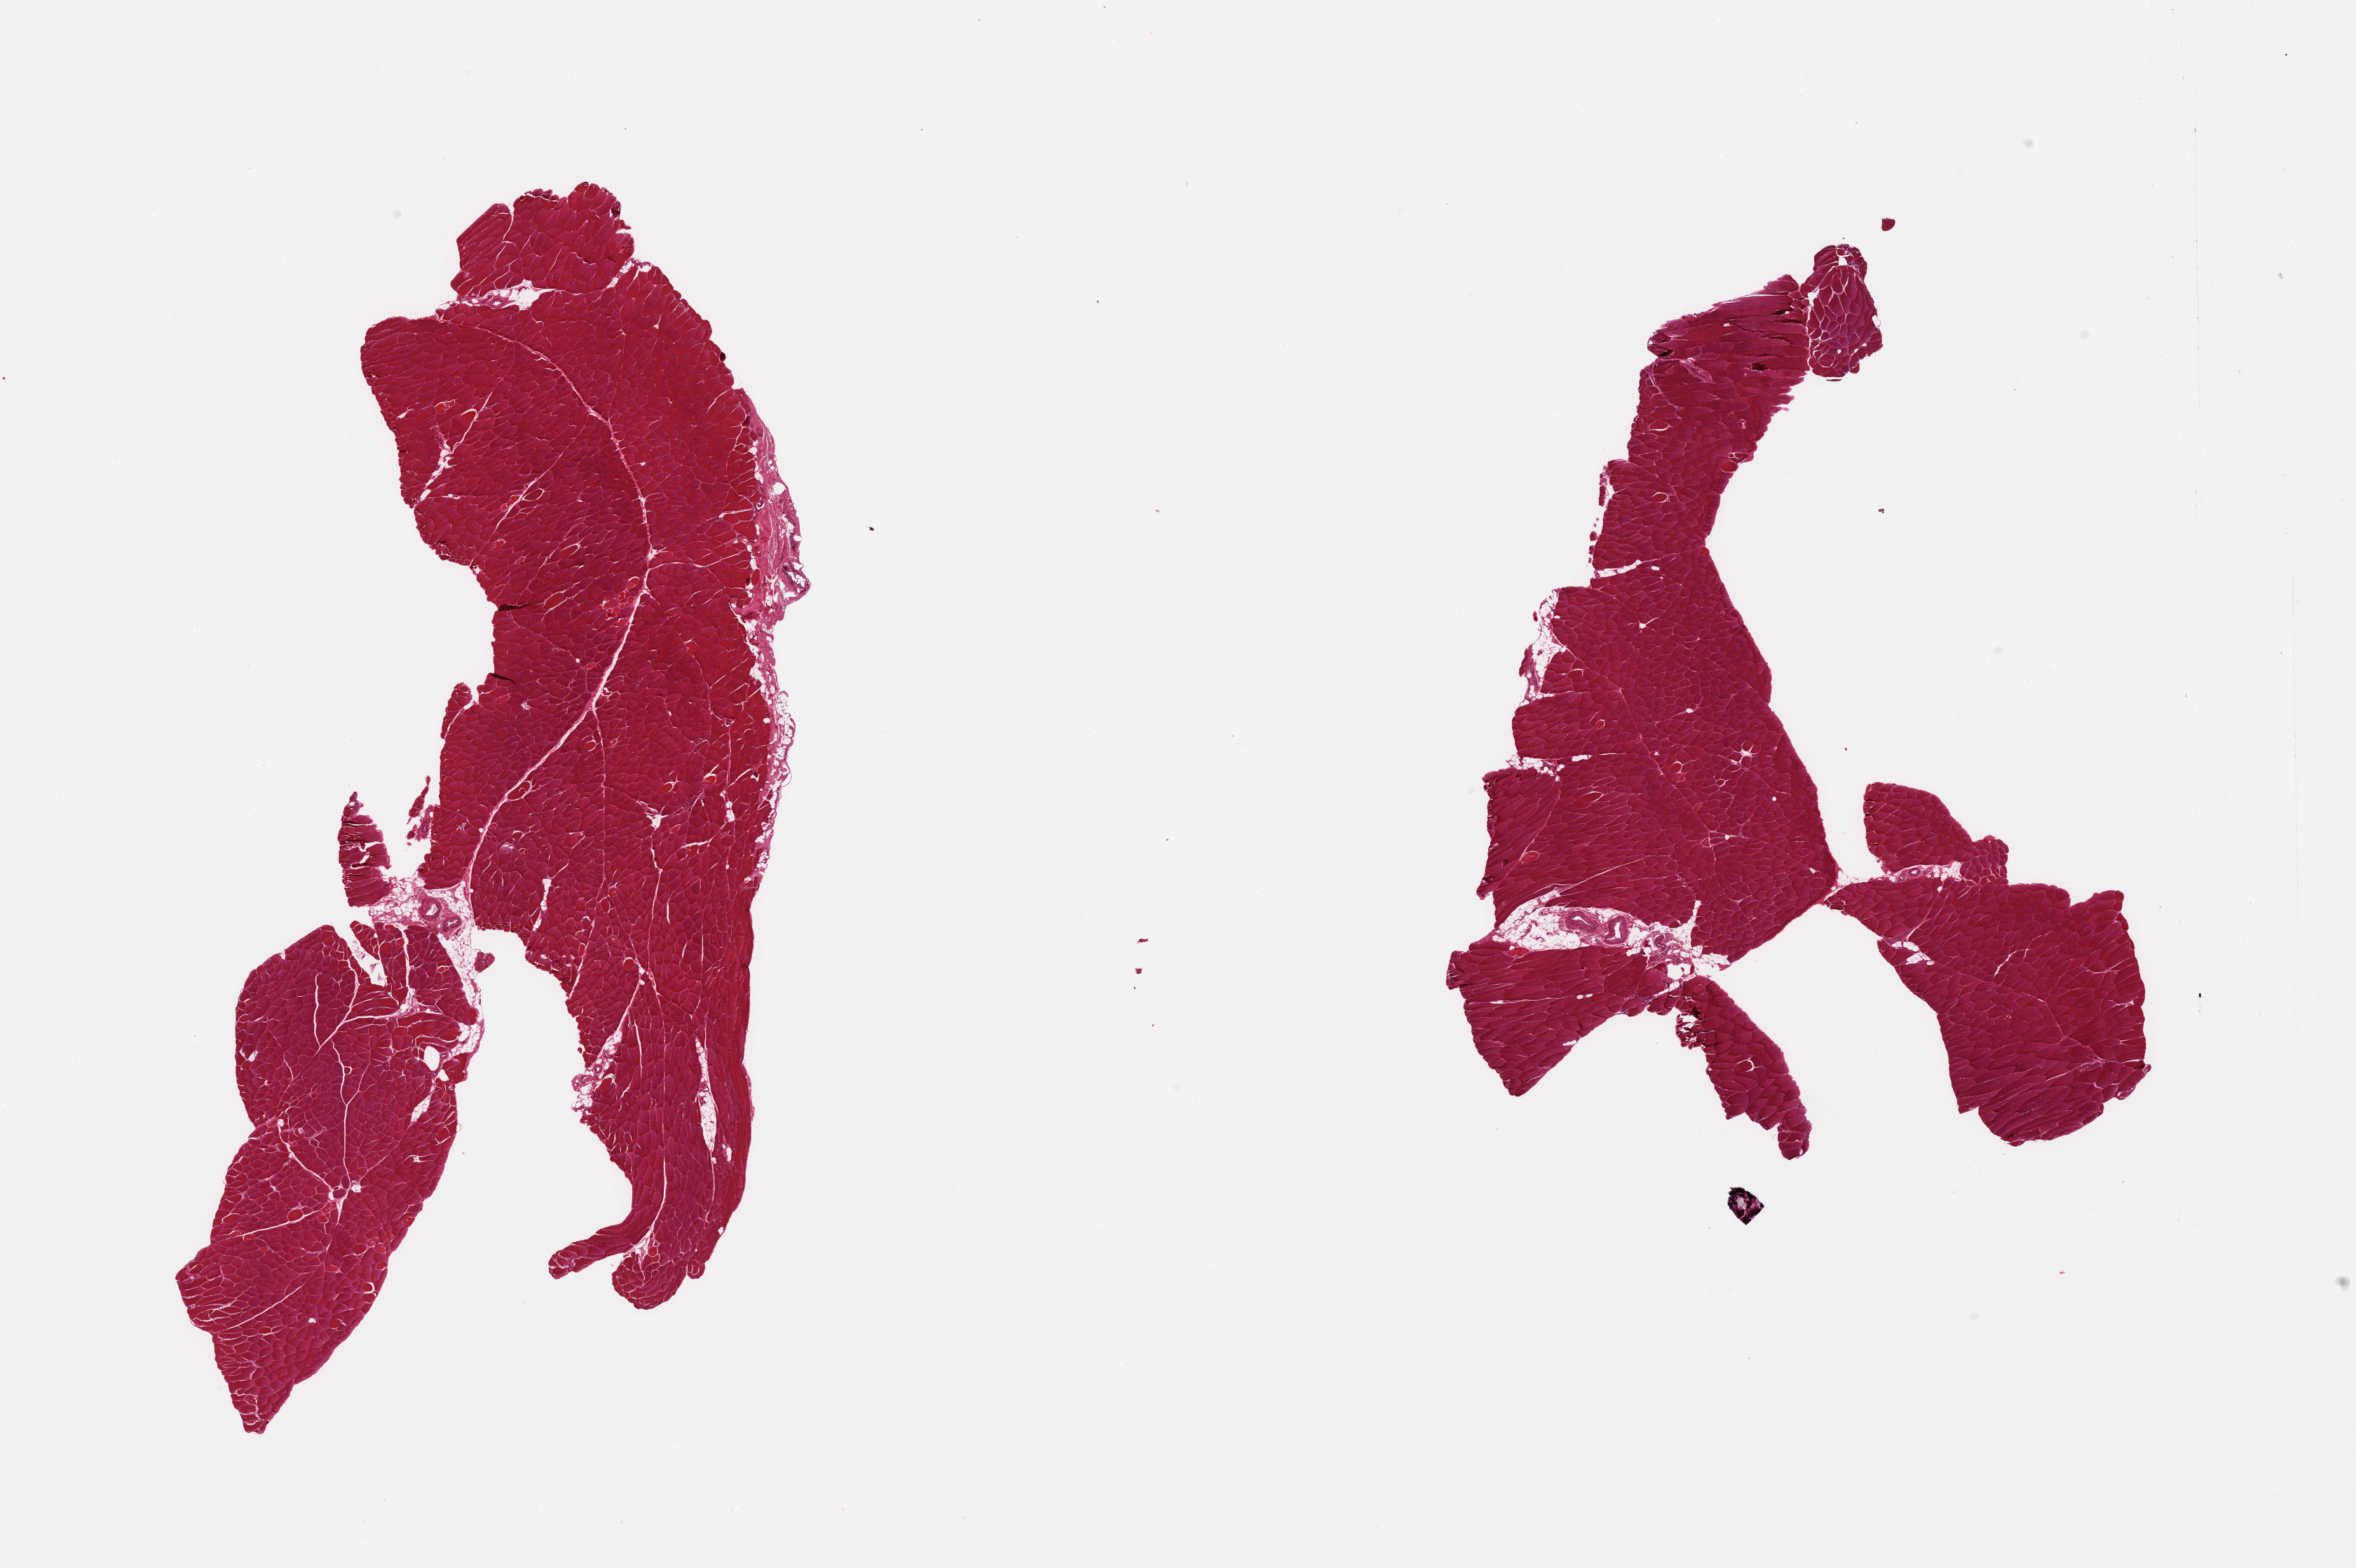
Whole-slide image, H&E stain — a low-resolution overview of the entire scanned area, about 26.6 x 17.7 mm (slide scanned at 20x). PAXgene-fixed, paraffin-embedded tissue. Sampled site (target tissue): skeletal muscle. Donor tissue sample. Male donor.
Reviewer comment on this tissue sample: 2 pieces; small amount of perivascular fat; rim of epimysium.